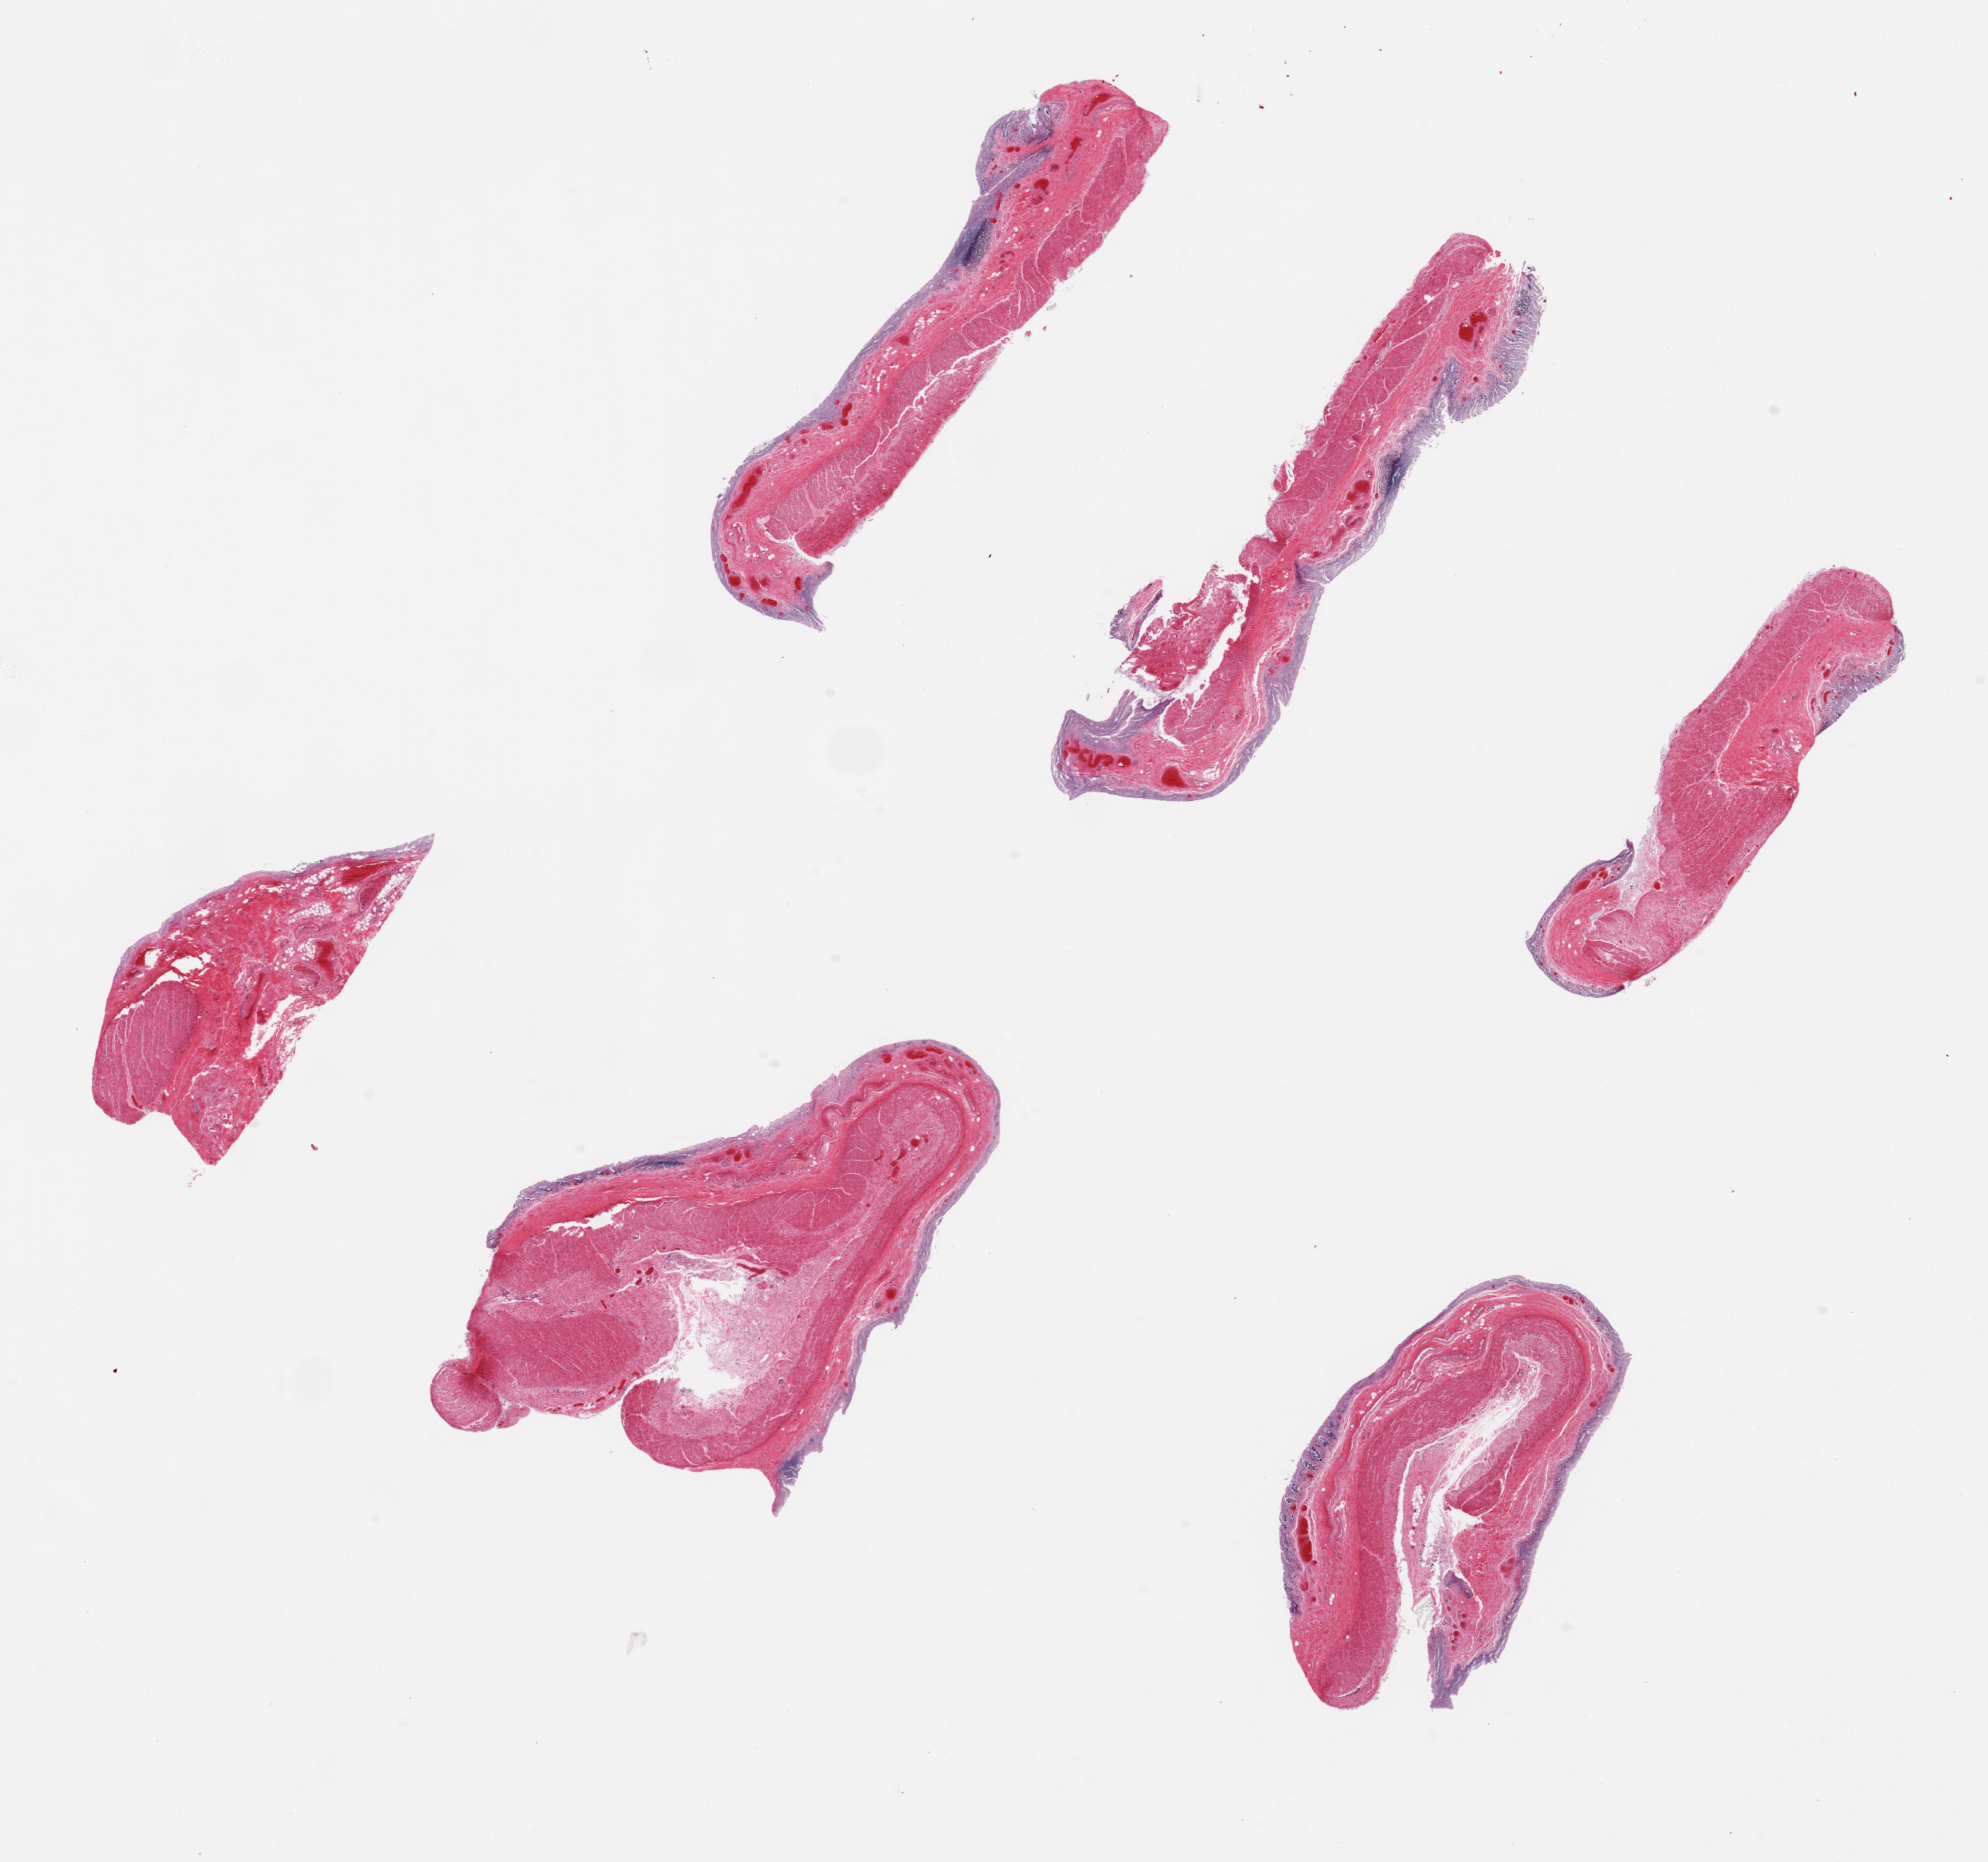
Digitized hematoxylin and eosin (H&E)-stained section — low-resolution overview of the scanned area, about 20.7 x 19.4 mm. PAXgene-fixed paraffin-embedded (PFPE) section. Sampled site (target tissue): transverse colon. Donor tissue sample.
Pathologist's review note for this sample: 6 pieces up to 7x4 mm; mucosa completely autolyzed, muscle moderately autolyzed.